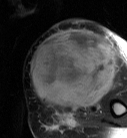
MRI of an extremity soft-tissue mass, one axial slice. Slice 27 of 87 in the series (ordered by position). T2-weighted fat-saturated. MR volume resampled by the dataset authors to the PET/CT grid (not the native acquisition matrix). 127 × 138 image matrix, field of view 124 × 135 mm. Female patient. From the clinical record (not read from this slice): histological type: pleiomorphic leiomyosarcoma; grade: high; site of the primary tumour: left biceps.
Annotated regions visible in this slice (expert contour drawn on MRI and transferred to this co-registered scan by the dataset authors):
- gross tumour volume including surrounding oedema: box from (x=29, y=30) to (x=115, y=110) px
- gross tumour volume (mass): (x=29, y=30)–(x=115, y=110)